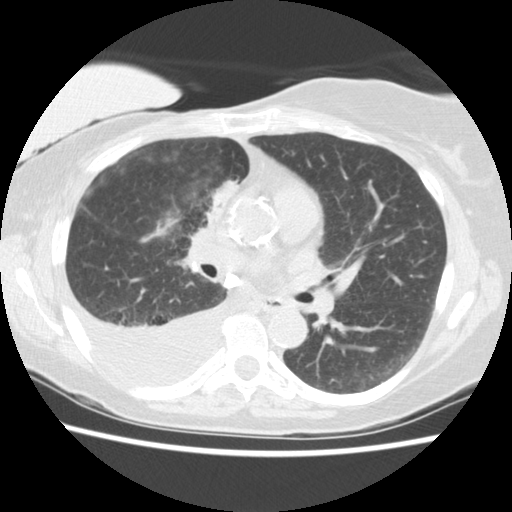
Chest CT (low-dose screening protocol), one axial image. Third screening round (two years after baseline). Lung window (W 1500 / L -600 HU). Standard (soft-tissue) reconstruction kernel (STANDARD). Slice 75 of 157 in the series. Female, age 56 years at enrolment. Current smoker at enrolment.
Expert reader's lesion annotation, bounding box <185,164,253,233> (left, top, right, bottom; pixels). The screening reader recorded 2 non-calcified nodules or masses ≥4 mm on this exam (right middle lobe, right lower lobe); which of them this box marks is not recorded. Official screen result: positive, other.